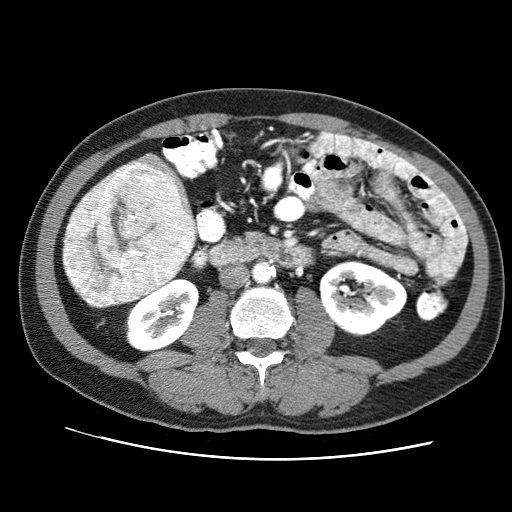
Contrast-enhanced abdominal CT (liver protocol), one axial slice; slice 18 of 71 in the series (ordered by position); reconstruction kernel STANDARD; soft-tissue window (W 400 / L 40 HU); 512 × 512 image matrix, field of view 360 × 360 mm. Case-level facts recorded for this patient, not image findings: diagnosis: hepatocellular carcinoma (patient treated with transarterial chemoembolisation; whether this scan precedes or follows treatment is not stated here); TNM stage (as recorded): Stage-II.
Structures marked on this image (semi-automatically segmented with operator editing):
- liver parenchyma outside the tumour (the mass and vessels are separate outlines, so this box may not span the whole liver): box from (x=64, y=152) to (x=195, y=308) px
- mass: (x=62, y=161)–(x=195, y=308)
- liver vessels: (x=184, y=199)–(x=193, y=247)